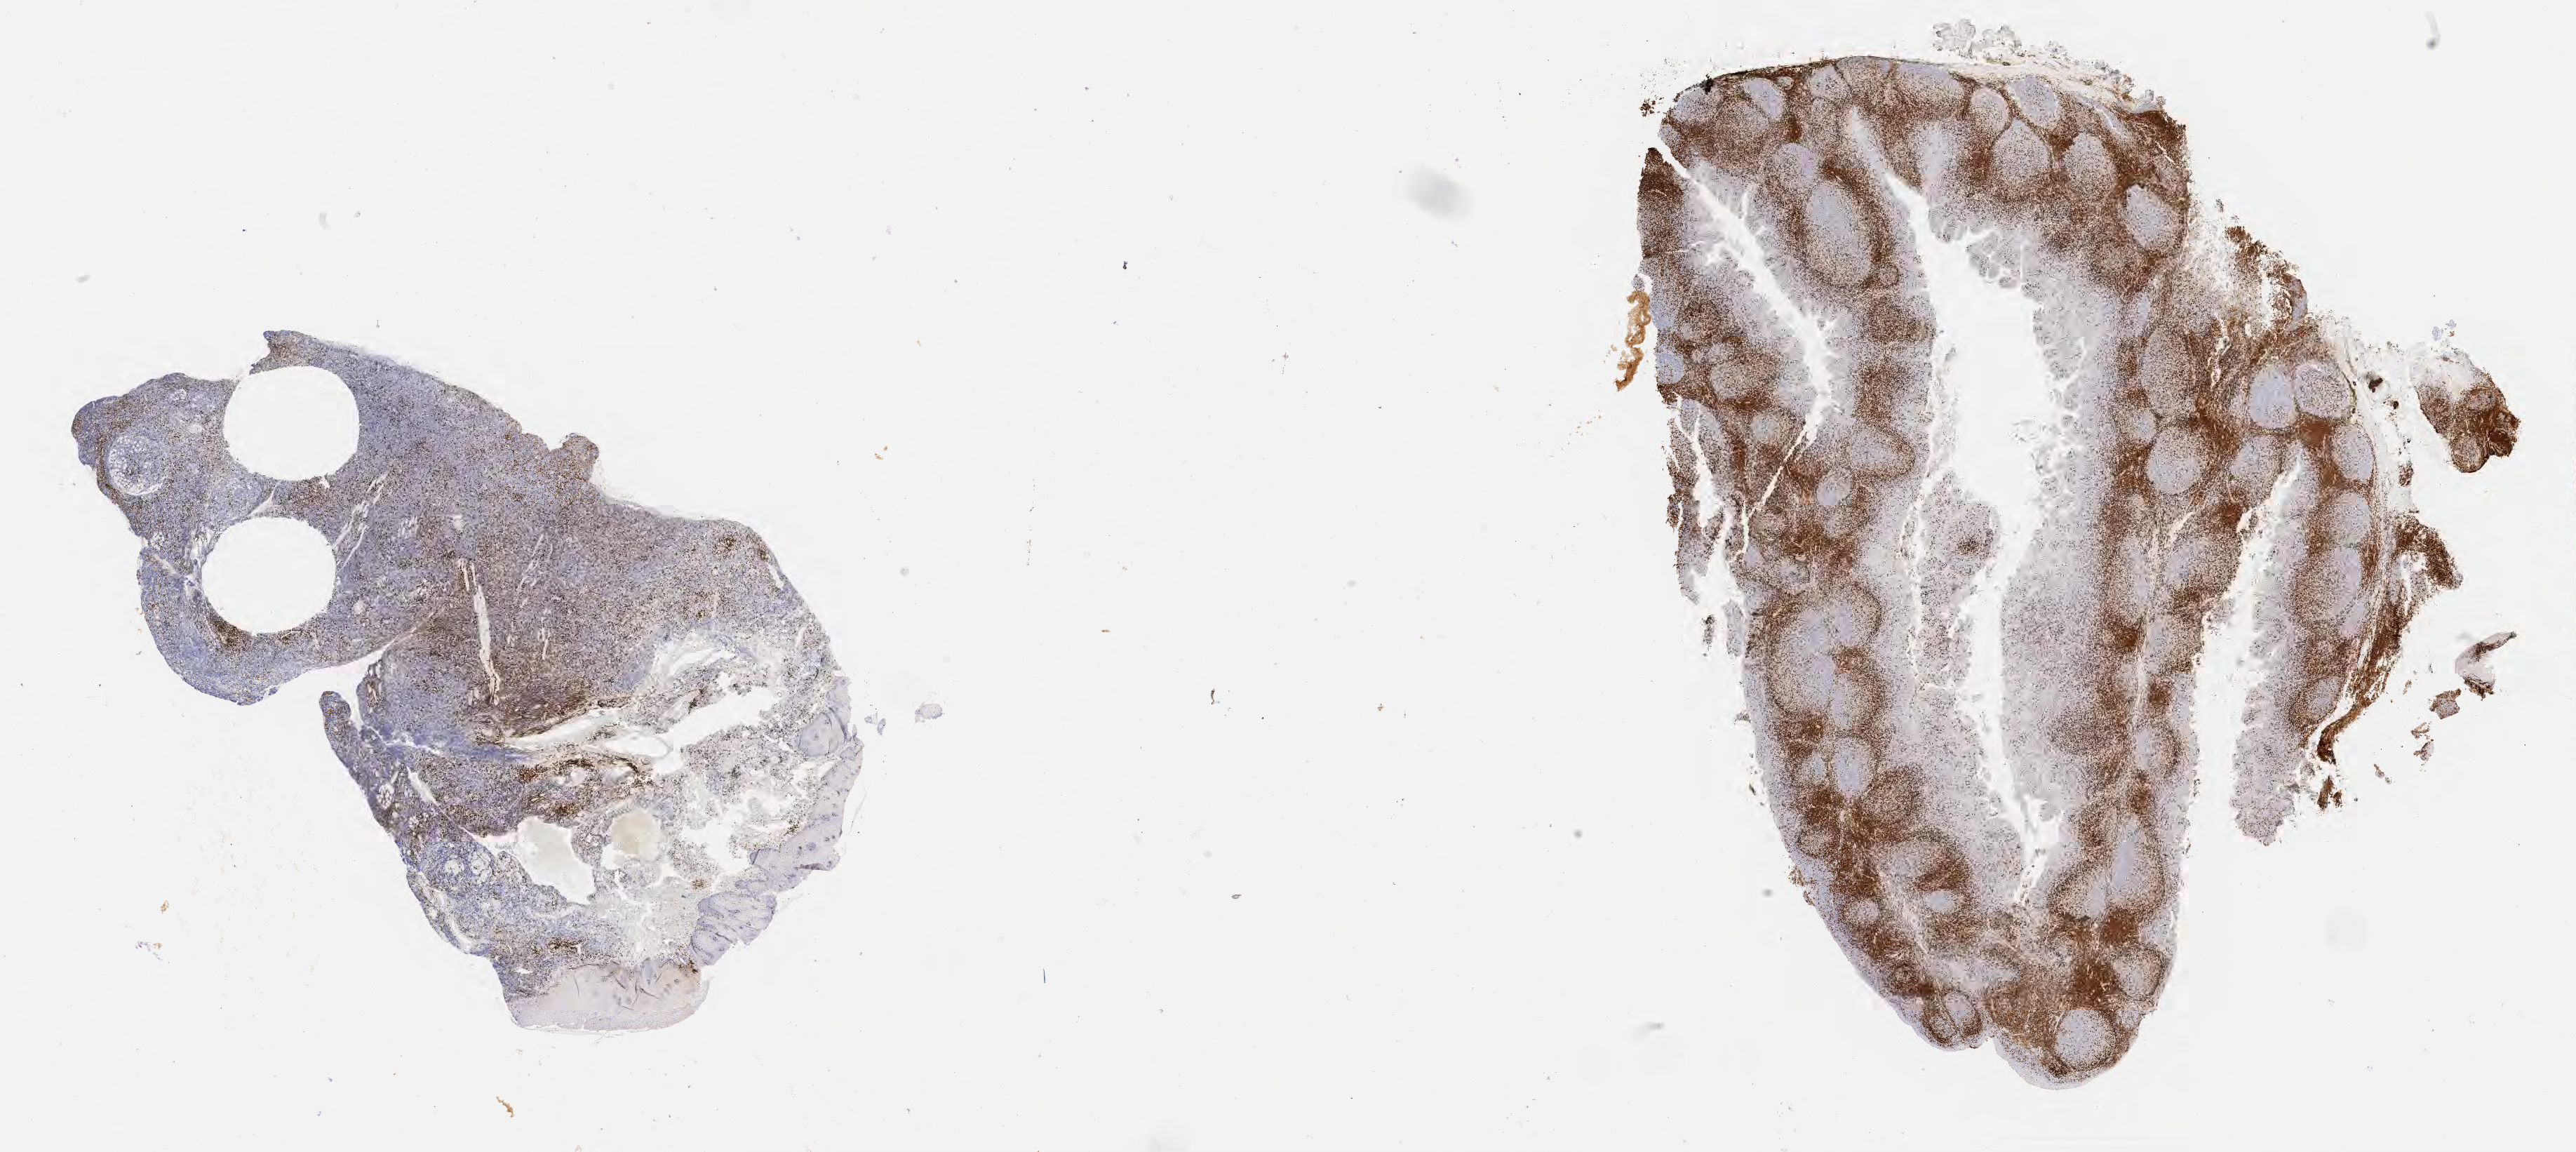
Immunohistochemistry (IHC) whole-slide image stained for CD3 — a low-resolution overview of the entire scanned area, about 29.7 x 13.3 mm. Tumor tissue. Anatomic site: cranium. Male, age 6 years at initial diagnosis.
* diagnosis: Burkitt lymphoma, NOS